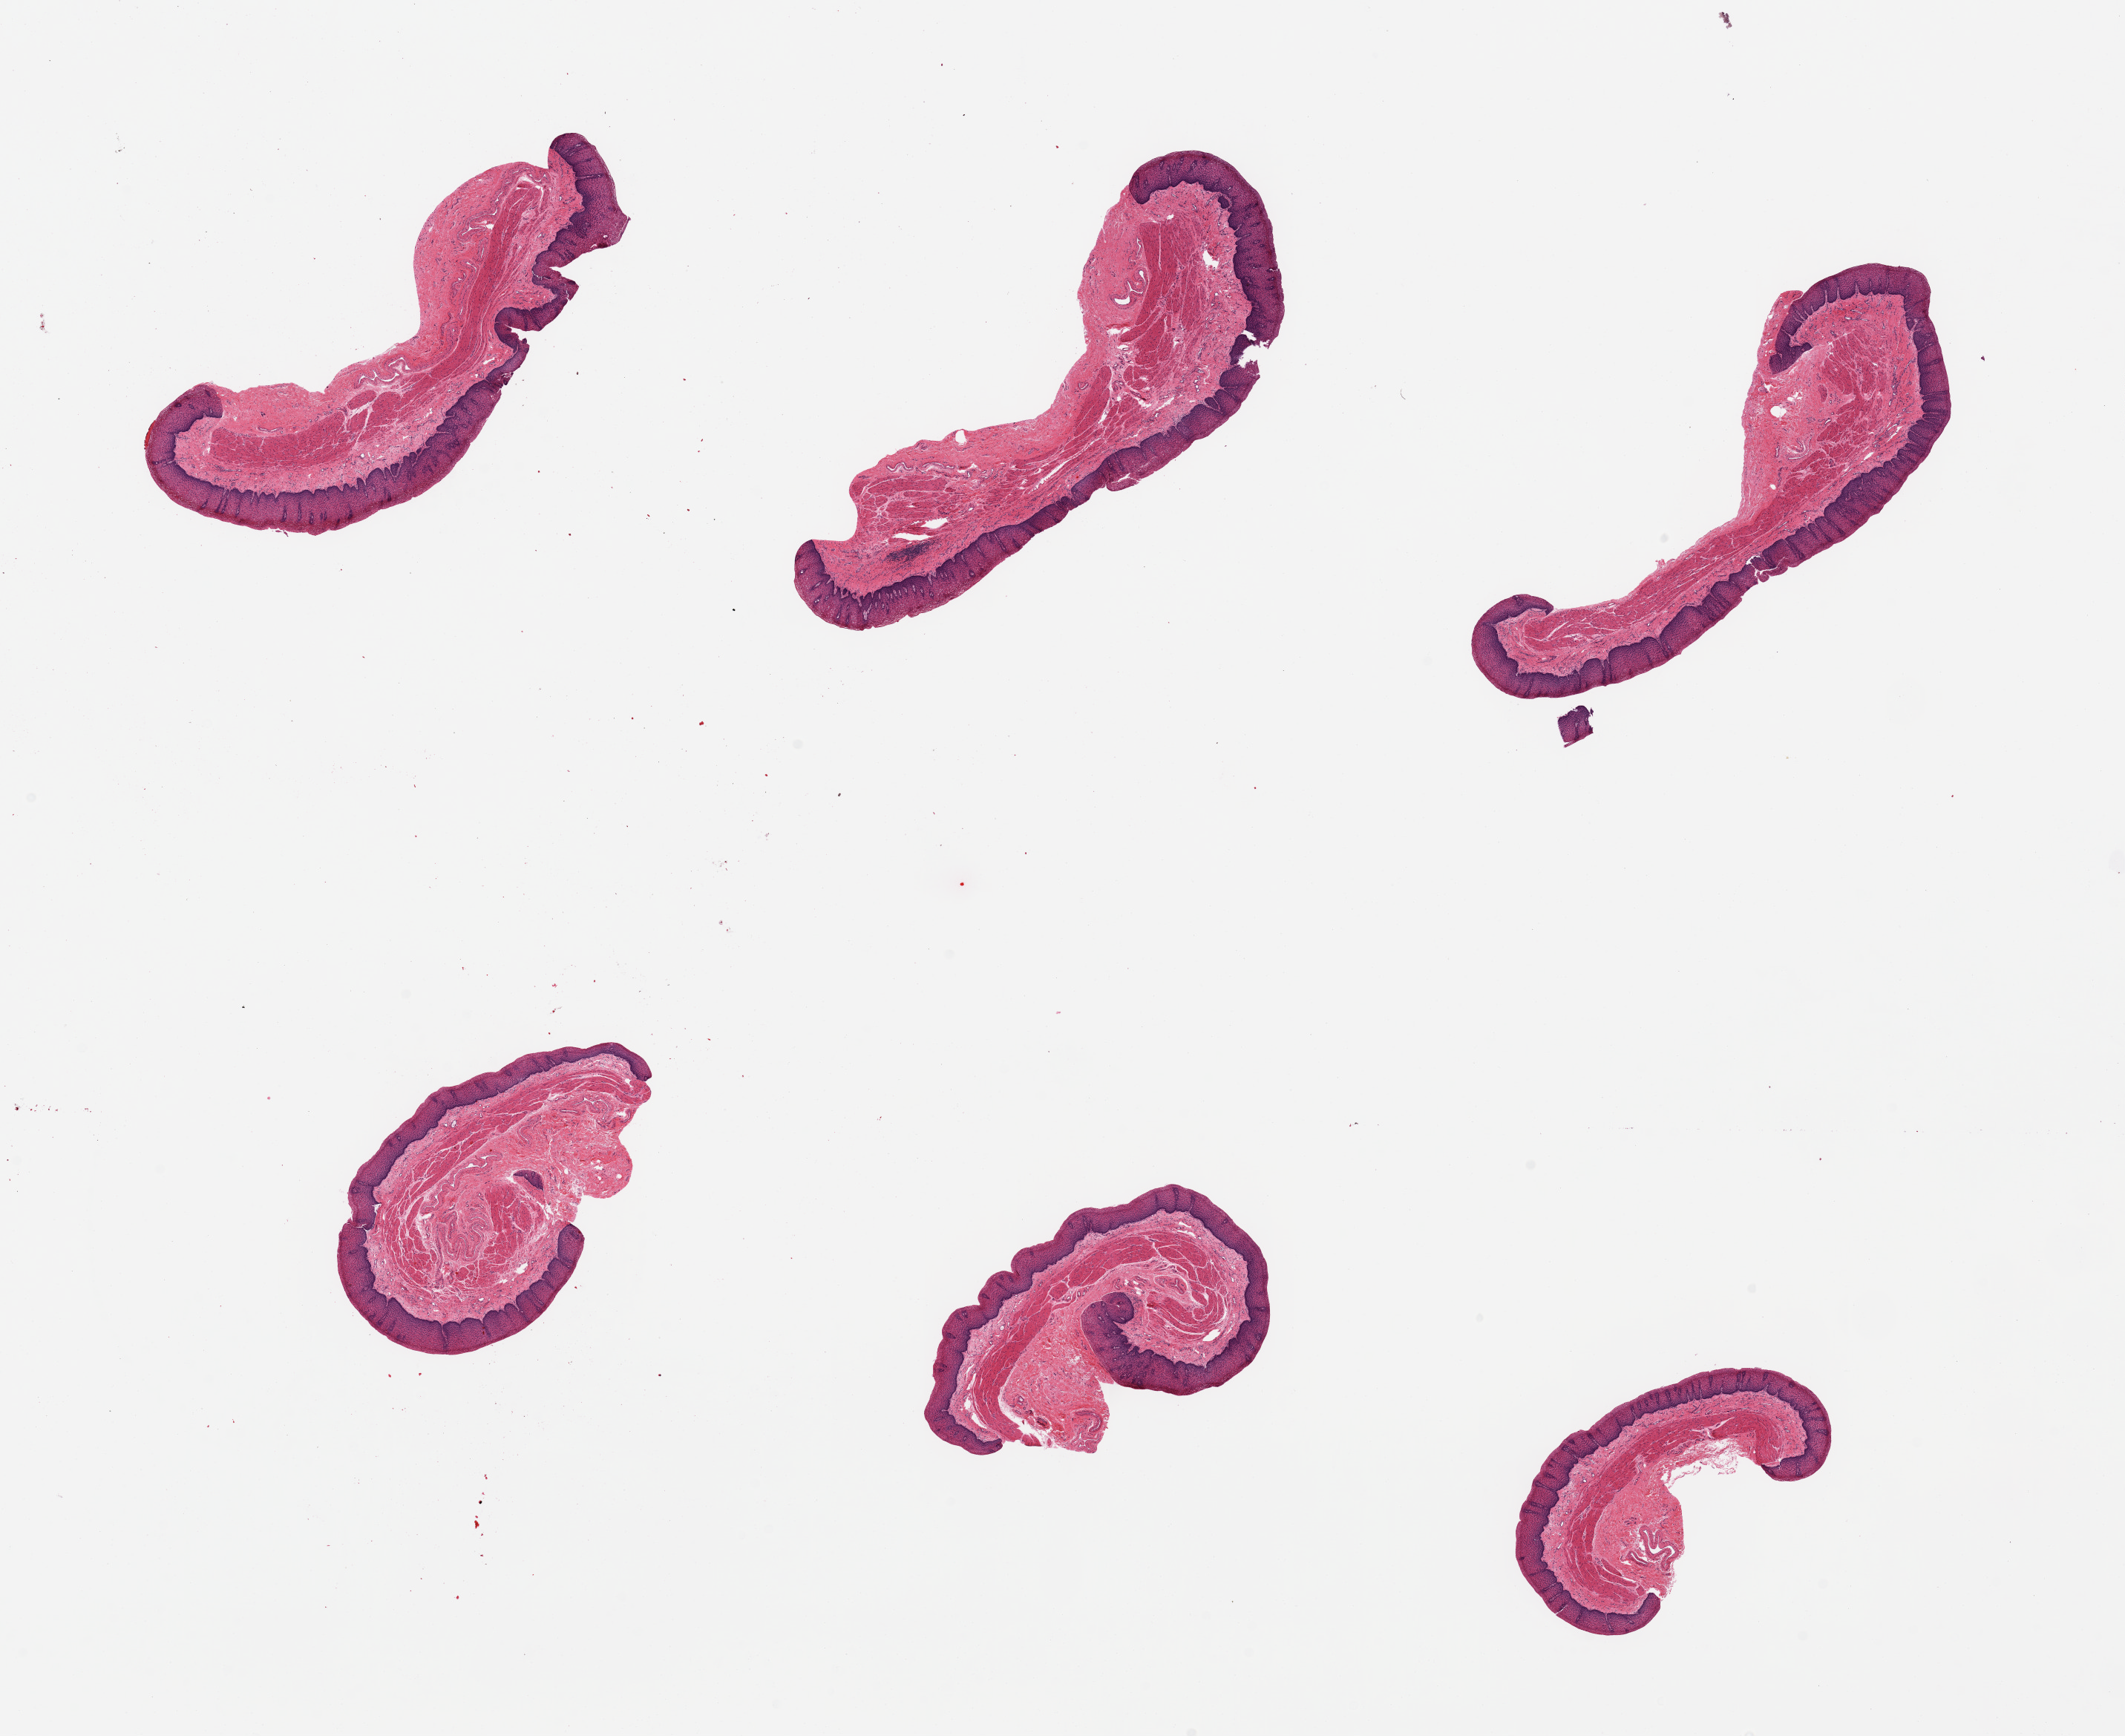
H&E whole-slide image, brightfield — shown as a low-resolution overview of the whole scanned area (about 22.6 x 18.5 mm, from a 20x scan); PAXgene-fixed paraffin-embedded (PFPE) section; target tissue: esophageal mucous membrane; donor tissue sample. Donor sex: female.
Pathologist's review note for this sample: 6 pieces, squamous mucosa well preserved; ~0.5mm, ~25% thickness.